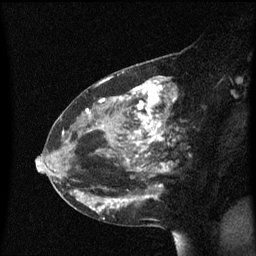
Breast MRI (dynamic contrast-enhanced), one sagittal slice. Dynamic contrast-enhanced series, image 2 of 3 at this slice position (ordered by acquisition). 1.5 T. TE 4.2 ms, TR 8.4 ms. 256 × 256 image matrix, field of view 200 × 200 mm. Female patient, age 48 years. From the clinical record (not read from this slice): setting: breast cancer imaged before/during neoadjuvant chemotherapy; receptor status: HR-positive, HER2-negative.
Outlined on this slice (semi-automatic segmentation, software-assisted and operator-edited):
- analysis volume of interest (the breast-tissue region the enhancement analysis was run in; not a lesion): bounding box <80,78,185,221> (left, top, right, bottom; pixels)
- tumour enhancement mask (voxels above the 70 % enhancement threshold inside the analysis volume of interest): <86,81,177,212>